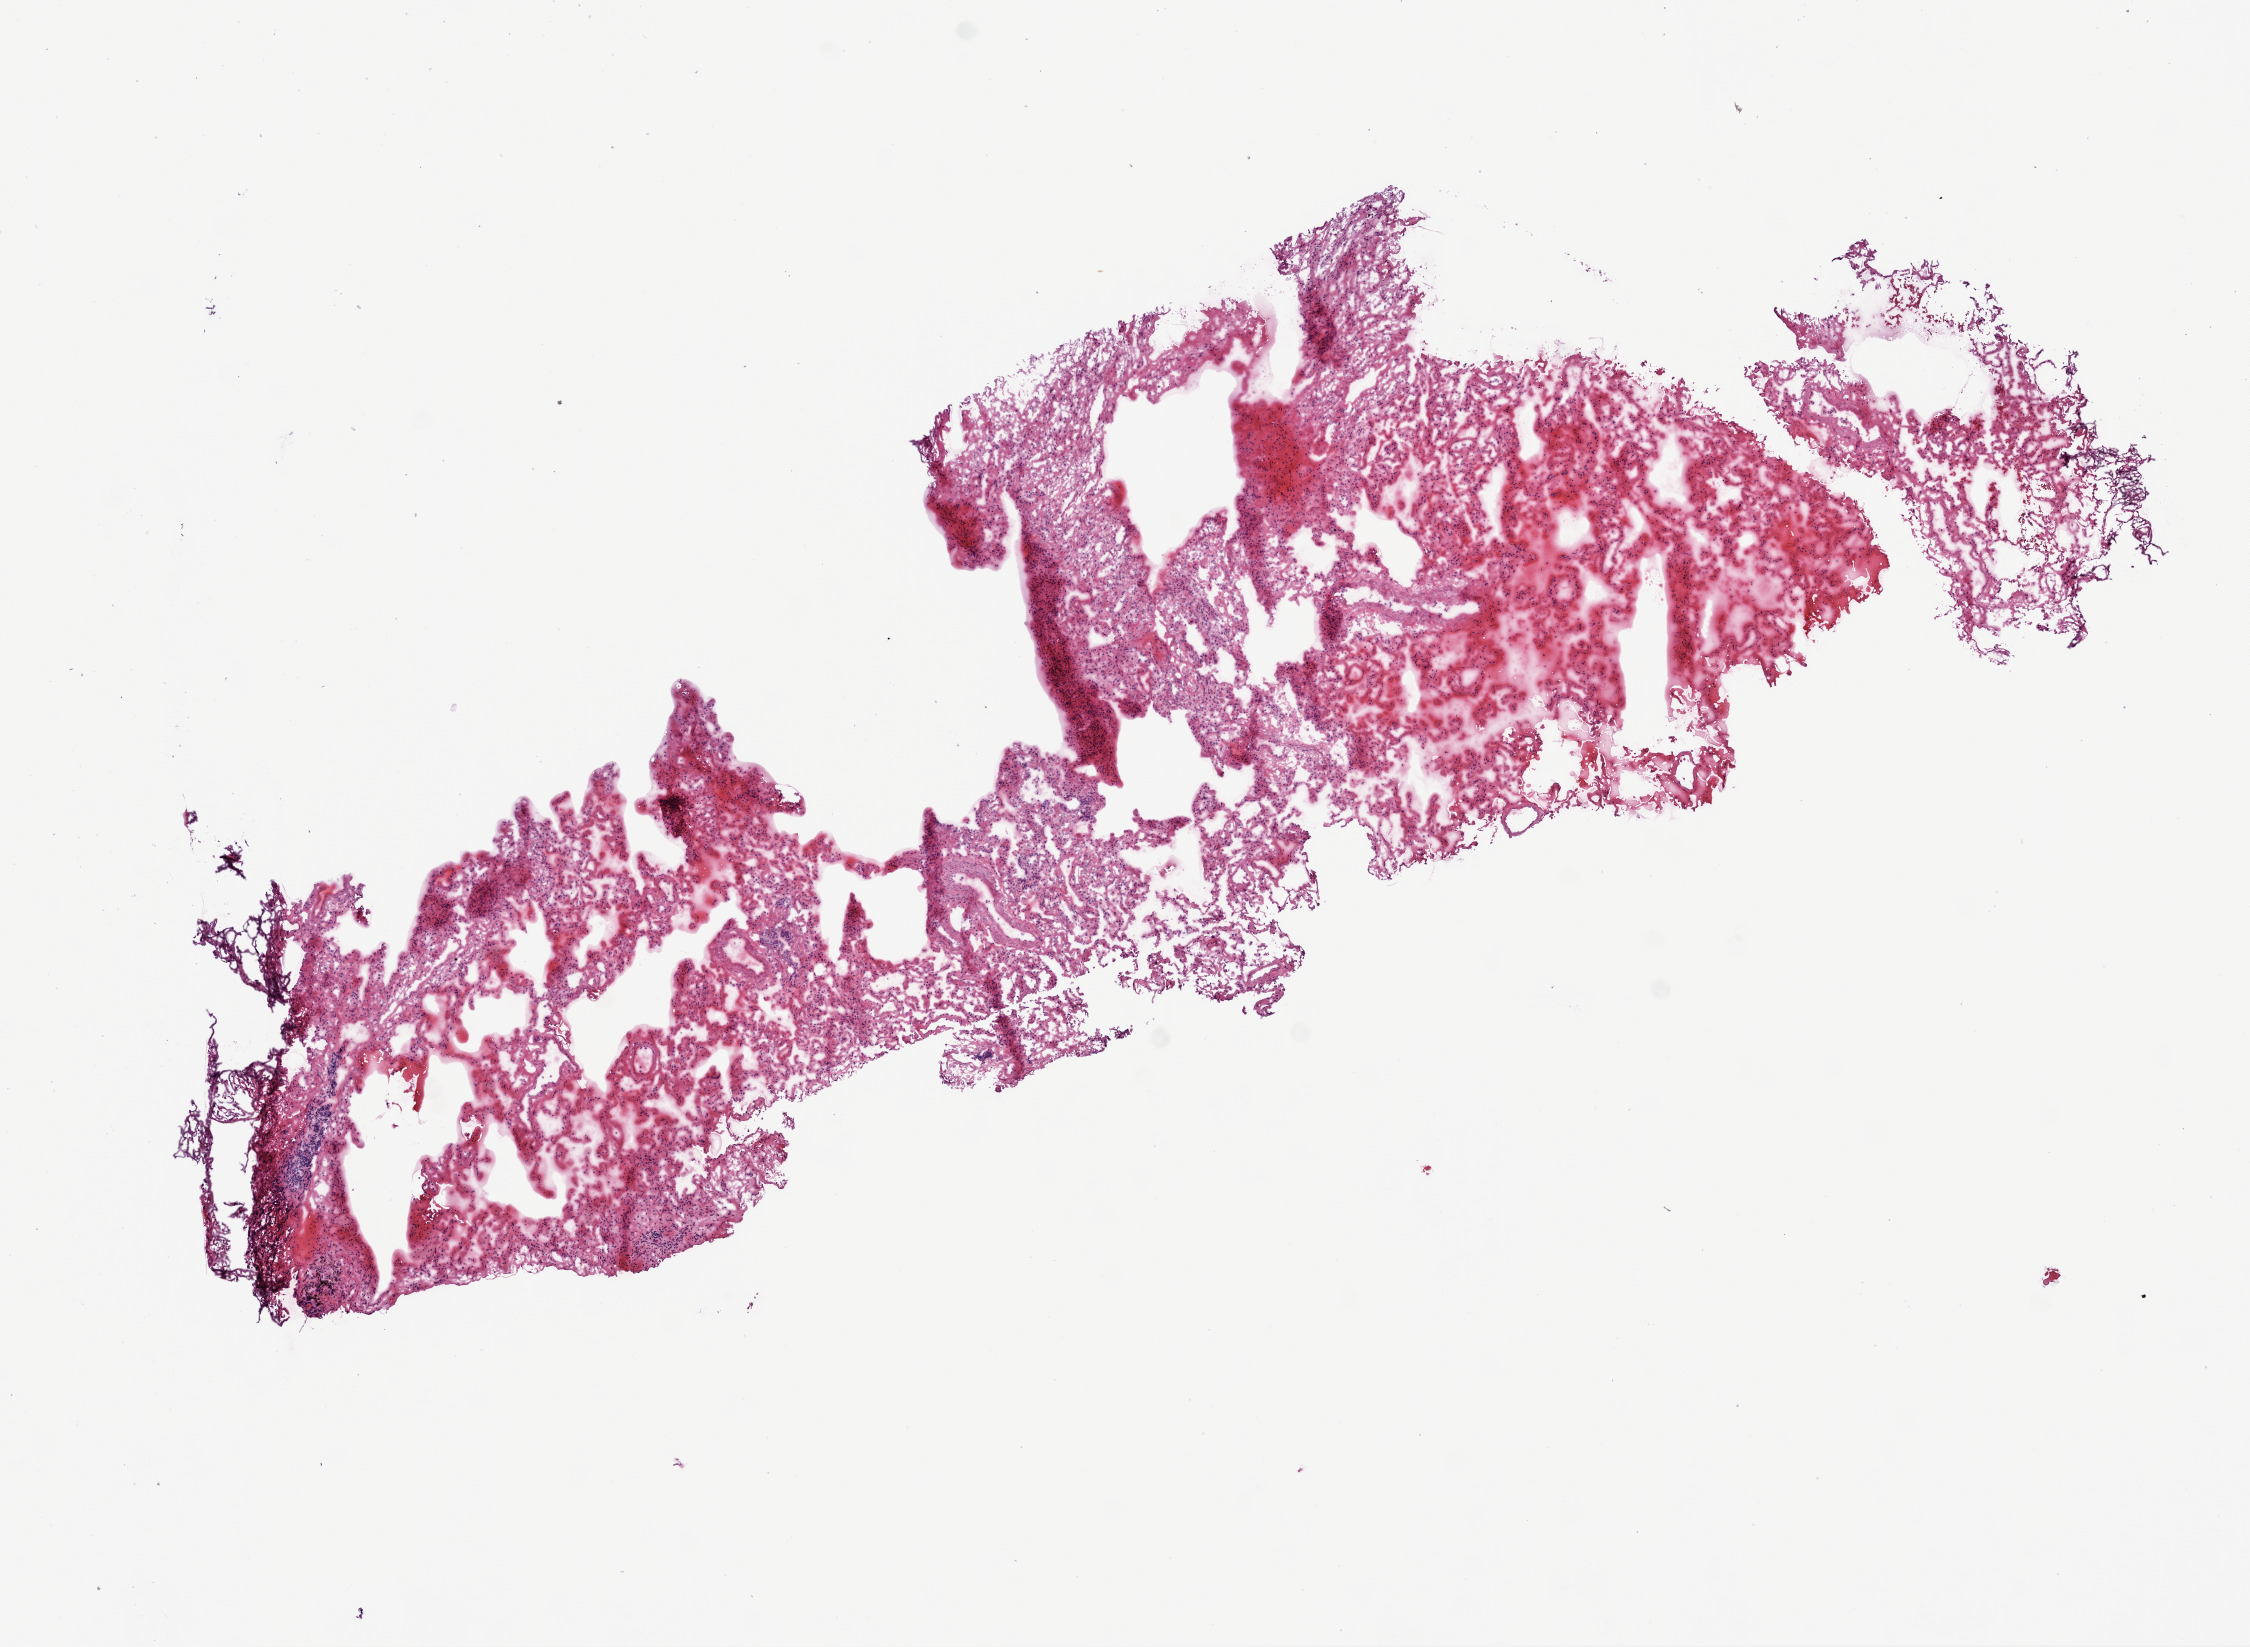
Whole-slide histology image, H&E, whole scanned area (about 9.0 x 6.6 mm, acquisition: 20x scan) shown as a low-resolution overview; frozen section from the bottom of the tissue portion; sample: solid tissue normal (non-tumour tissue), lung. Female patient; age at initial diagnosis 69 years.
This section: solid tissue normal (non-tumour) sample from the same patient. Patient diagnosis: Adenocarcinoma, NOS (upper lobe, lung).